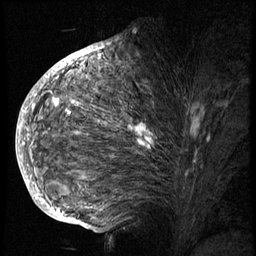
Breast MRI (dynamic contrast-enhanced), one sagittal slice. Position 41 of 74 along the scan axis. 3 images stored at this slice position (order not interpretable as contrast timing). 1.5 T. TE 4.2 ms, TR 8.9 ms. 256 × 256 image matrix. Female patient, age 57 years. Case-level facts recorded for this patient, not image findings: setting: breast cancer imaged before/during neoadjuvant chemotherapy; receptor status: HER2-positive.
Structures marked on this image (semi-automatically segmented with operator editing):
- analysis volume of interest (the breast-tissue region the enhancement analysis was run in; not a lesion): bounding box [x1, y1, x2, y2] px = [40, 62, 242, 175]
- tumour enhancement mask (voxels above the 140 % enhancement threshold inside the analysis volume of interest): [53, 91, 155, 150]